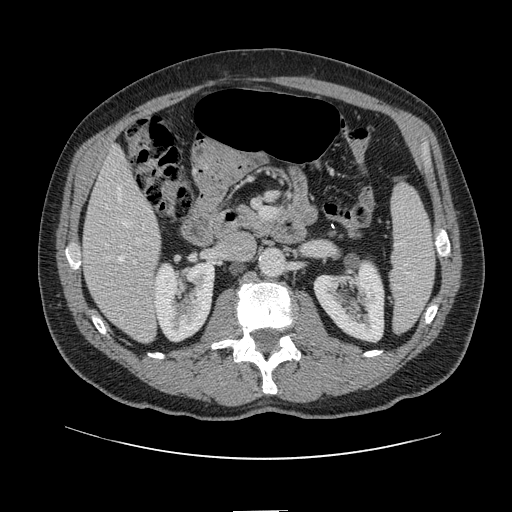
Contrast-enhanced abdominal CT, one axial slice. Slice 45 of 161 in the series (ordered by position). 120 kVp. Intravenous contrast given. Soft-tissue window (W 400 / L 40 HU). 2.5 mm slice thickness. 512 × 512 image matrix. Male patient, age 66 years. From the clinical record (not read from this slice): diagnosis: colorectal cancer liver metastases, imaged before liver resection; multiple liver metastases: no.
Annotated regions visible in this slice (outlined manually by an expert reader):
- hepatic veins: bounding box (x1, y1, x2, y2) in pixels: (119, 187, 127, 262)
- liver: (83, 151, 159, 342)
- planned liver remnant (the part of the liver to remain after resection): (83, 151, 156, 273)